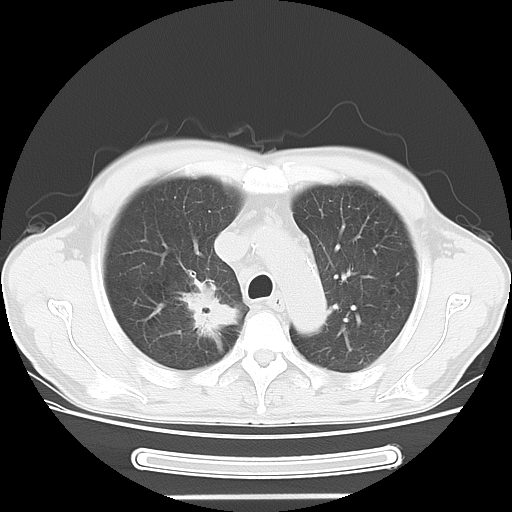
Chest CT, one axial slice. Position 37 of 51 along the scan axis. Reconstruction kernel LUNG. 120 kVp. Lung window (W 1500 / L -600 HU). 512 × 512 image matrix, field of view 350 × 350 mm. Male patient, age 57 years. Case-level facts recorded for this patient, not image findings: clinical TNM (as recorded): T2 N3 M1b.
Structures marked on this image (bounding box drawn by a radiologist):
- lung tumour (recorded histology: adenocarcinoma): bounding box <178,267,234,340> (left, top, right, bottom; pixels)